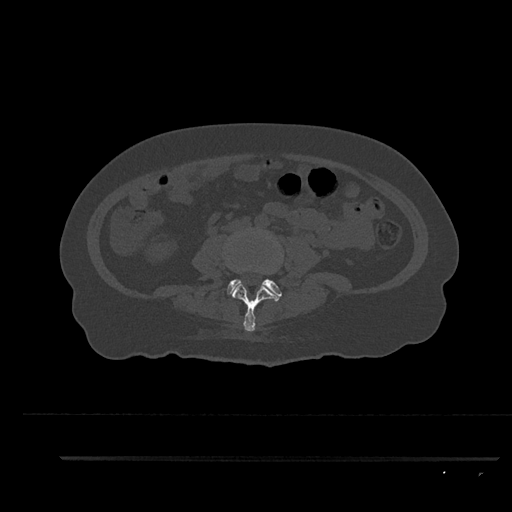
CT including the spine, one axial slice; position 55 of 797 along the scan axis; bone window (W 1800 / L 400 HU); 0.5 mm slice thickness; 512 × 512 image matrix. Female patient, age 44 years. From the clinical record (not read from this slice): primary cancer: renal; vertebrae with lytic lesions (as recorded): L1.
Structures marked on this image (semi-automatic segmentation, software-assisted and operator-edited):
- L3 vertebra: bounding box [x1, y1, x2, y2] px = [231, 282, 282, 331]
- L4 vertebra: [225, 279, 282, 296]